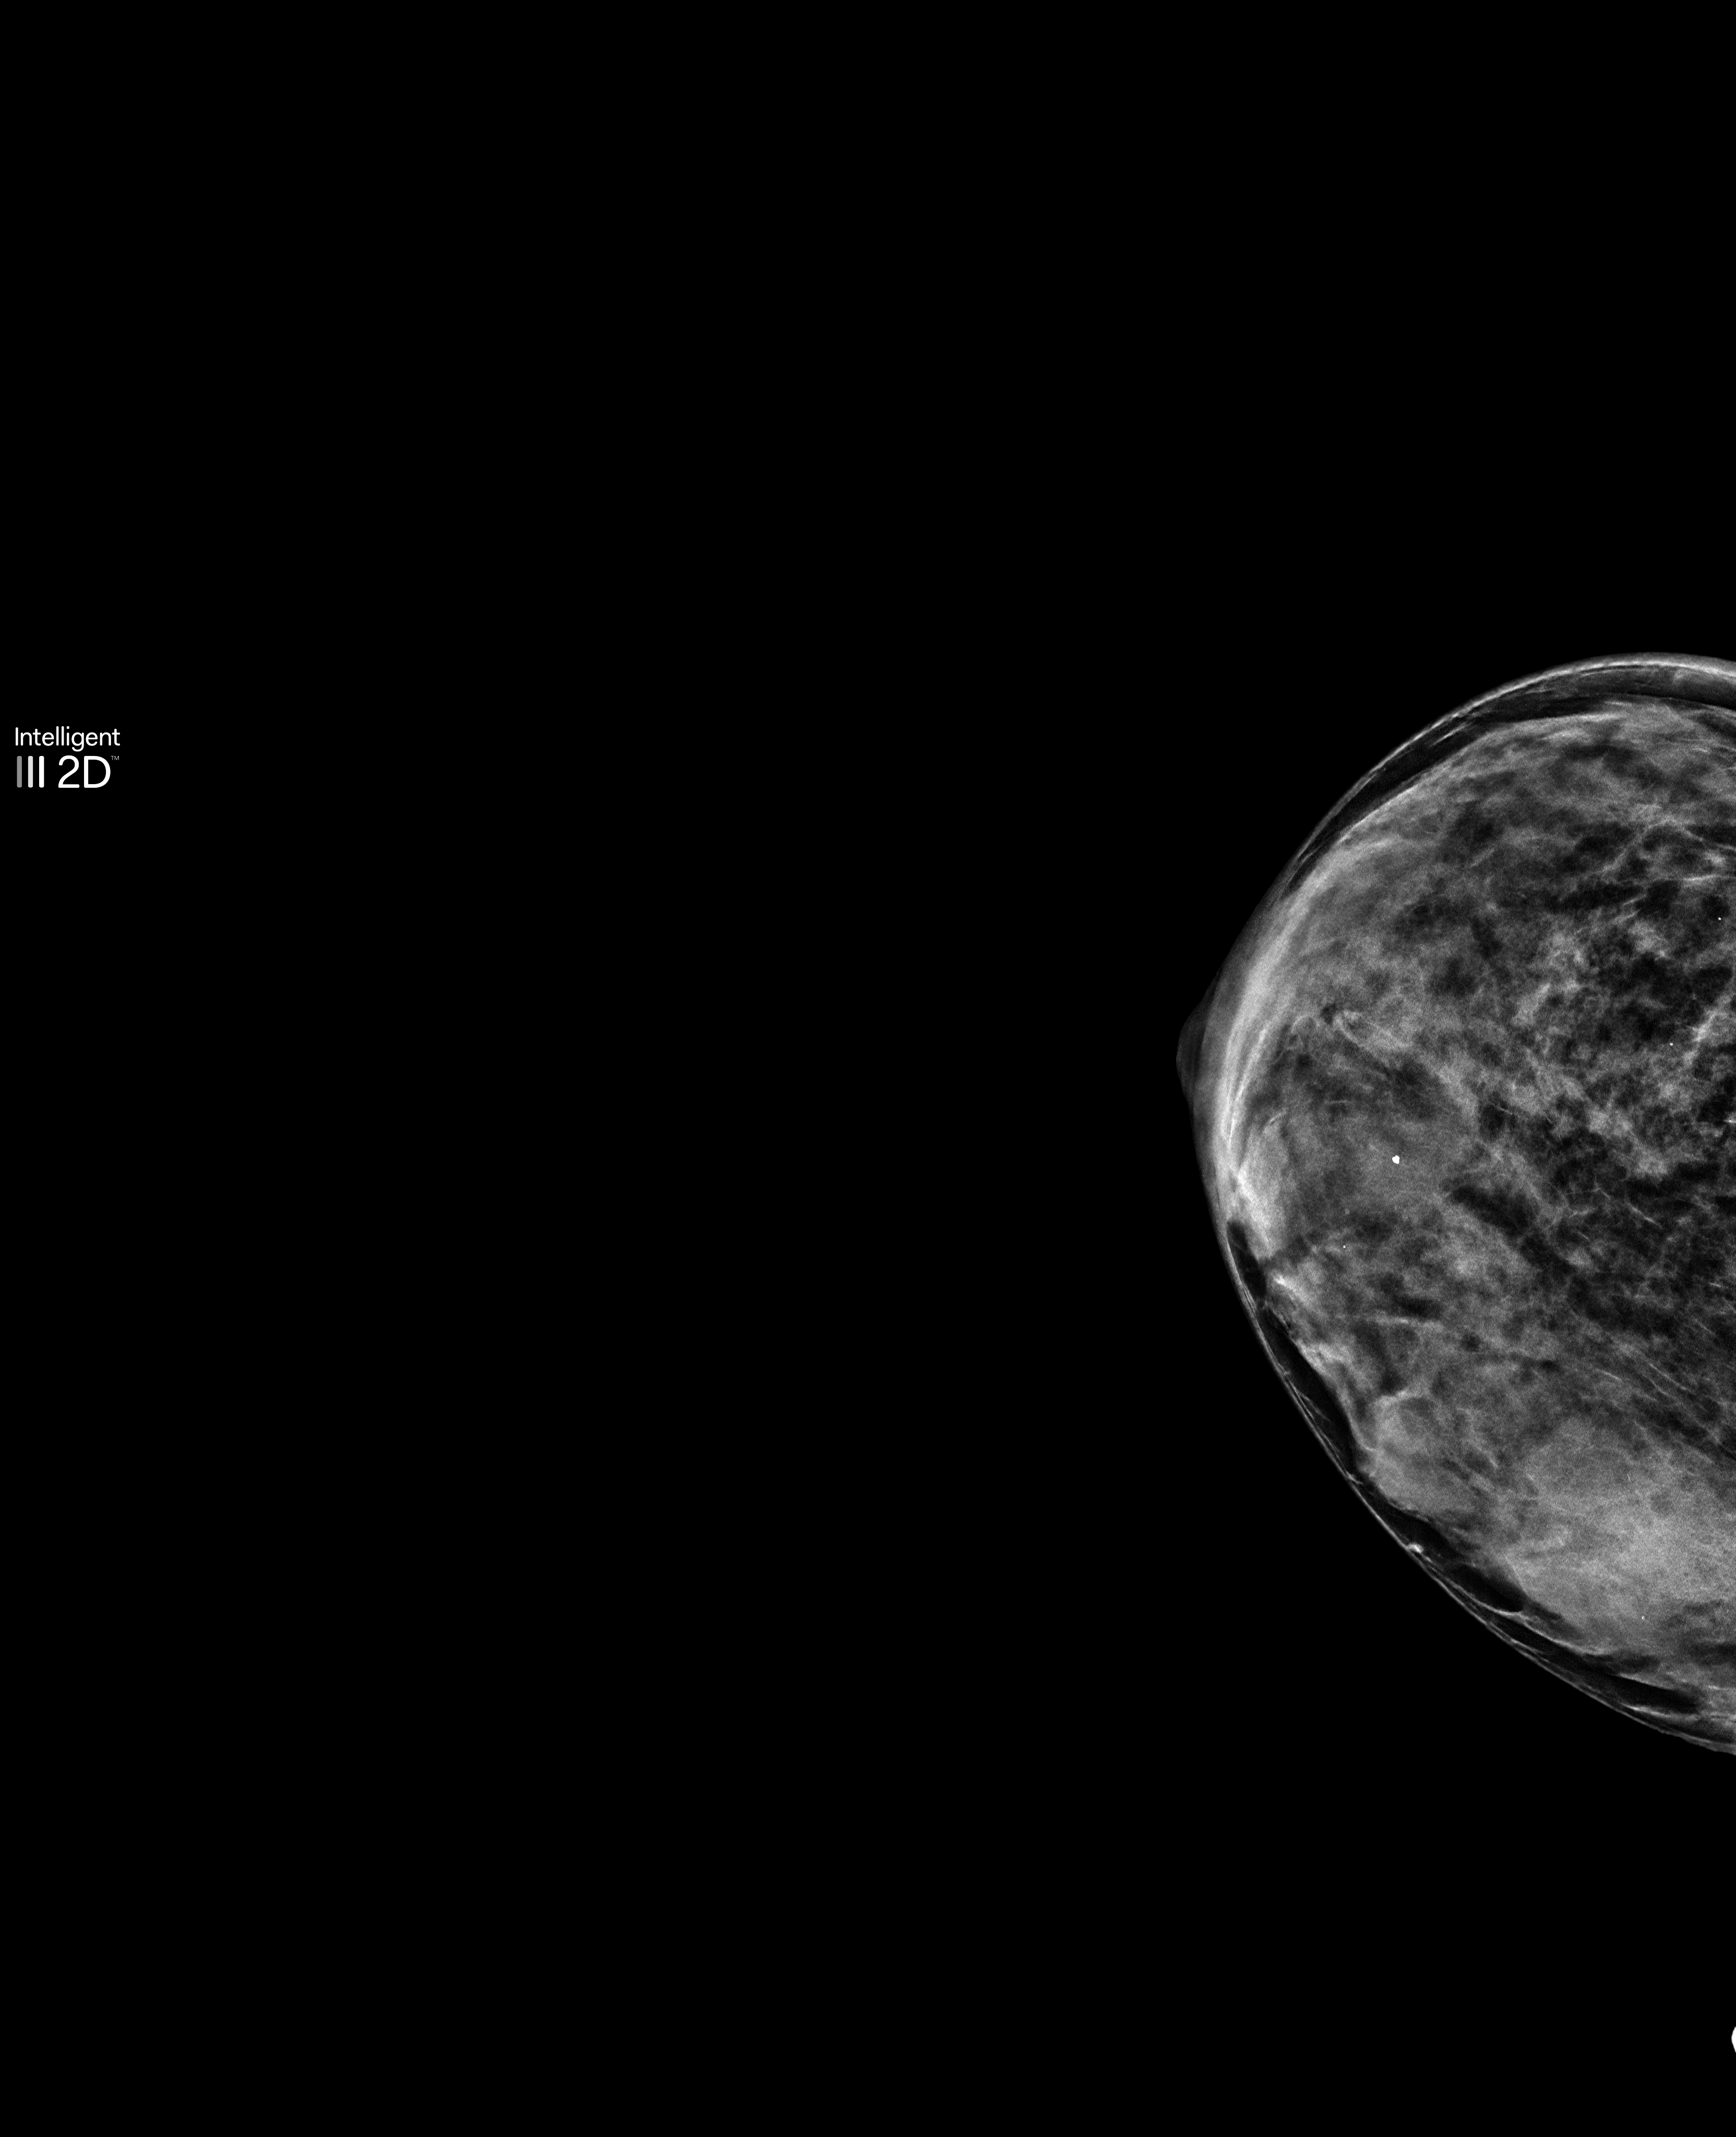
Screening examination; system: Selenia Dimensions. Female patient, age 53 years.
Image type: synthesized 2-D view from tomosynthesis. Breast: right. Projection: craniocaudal (CC) view.